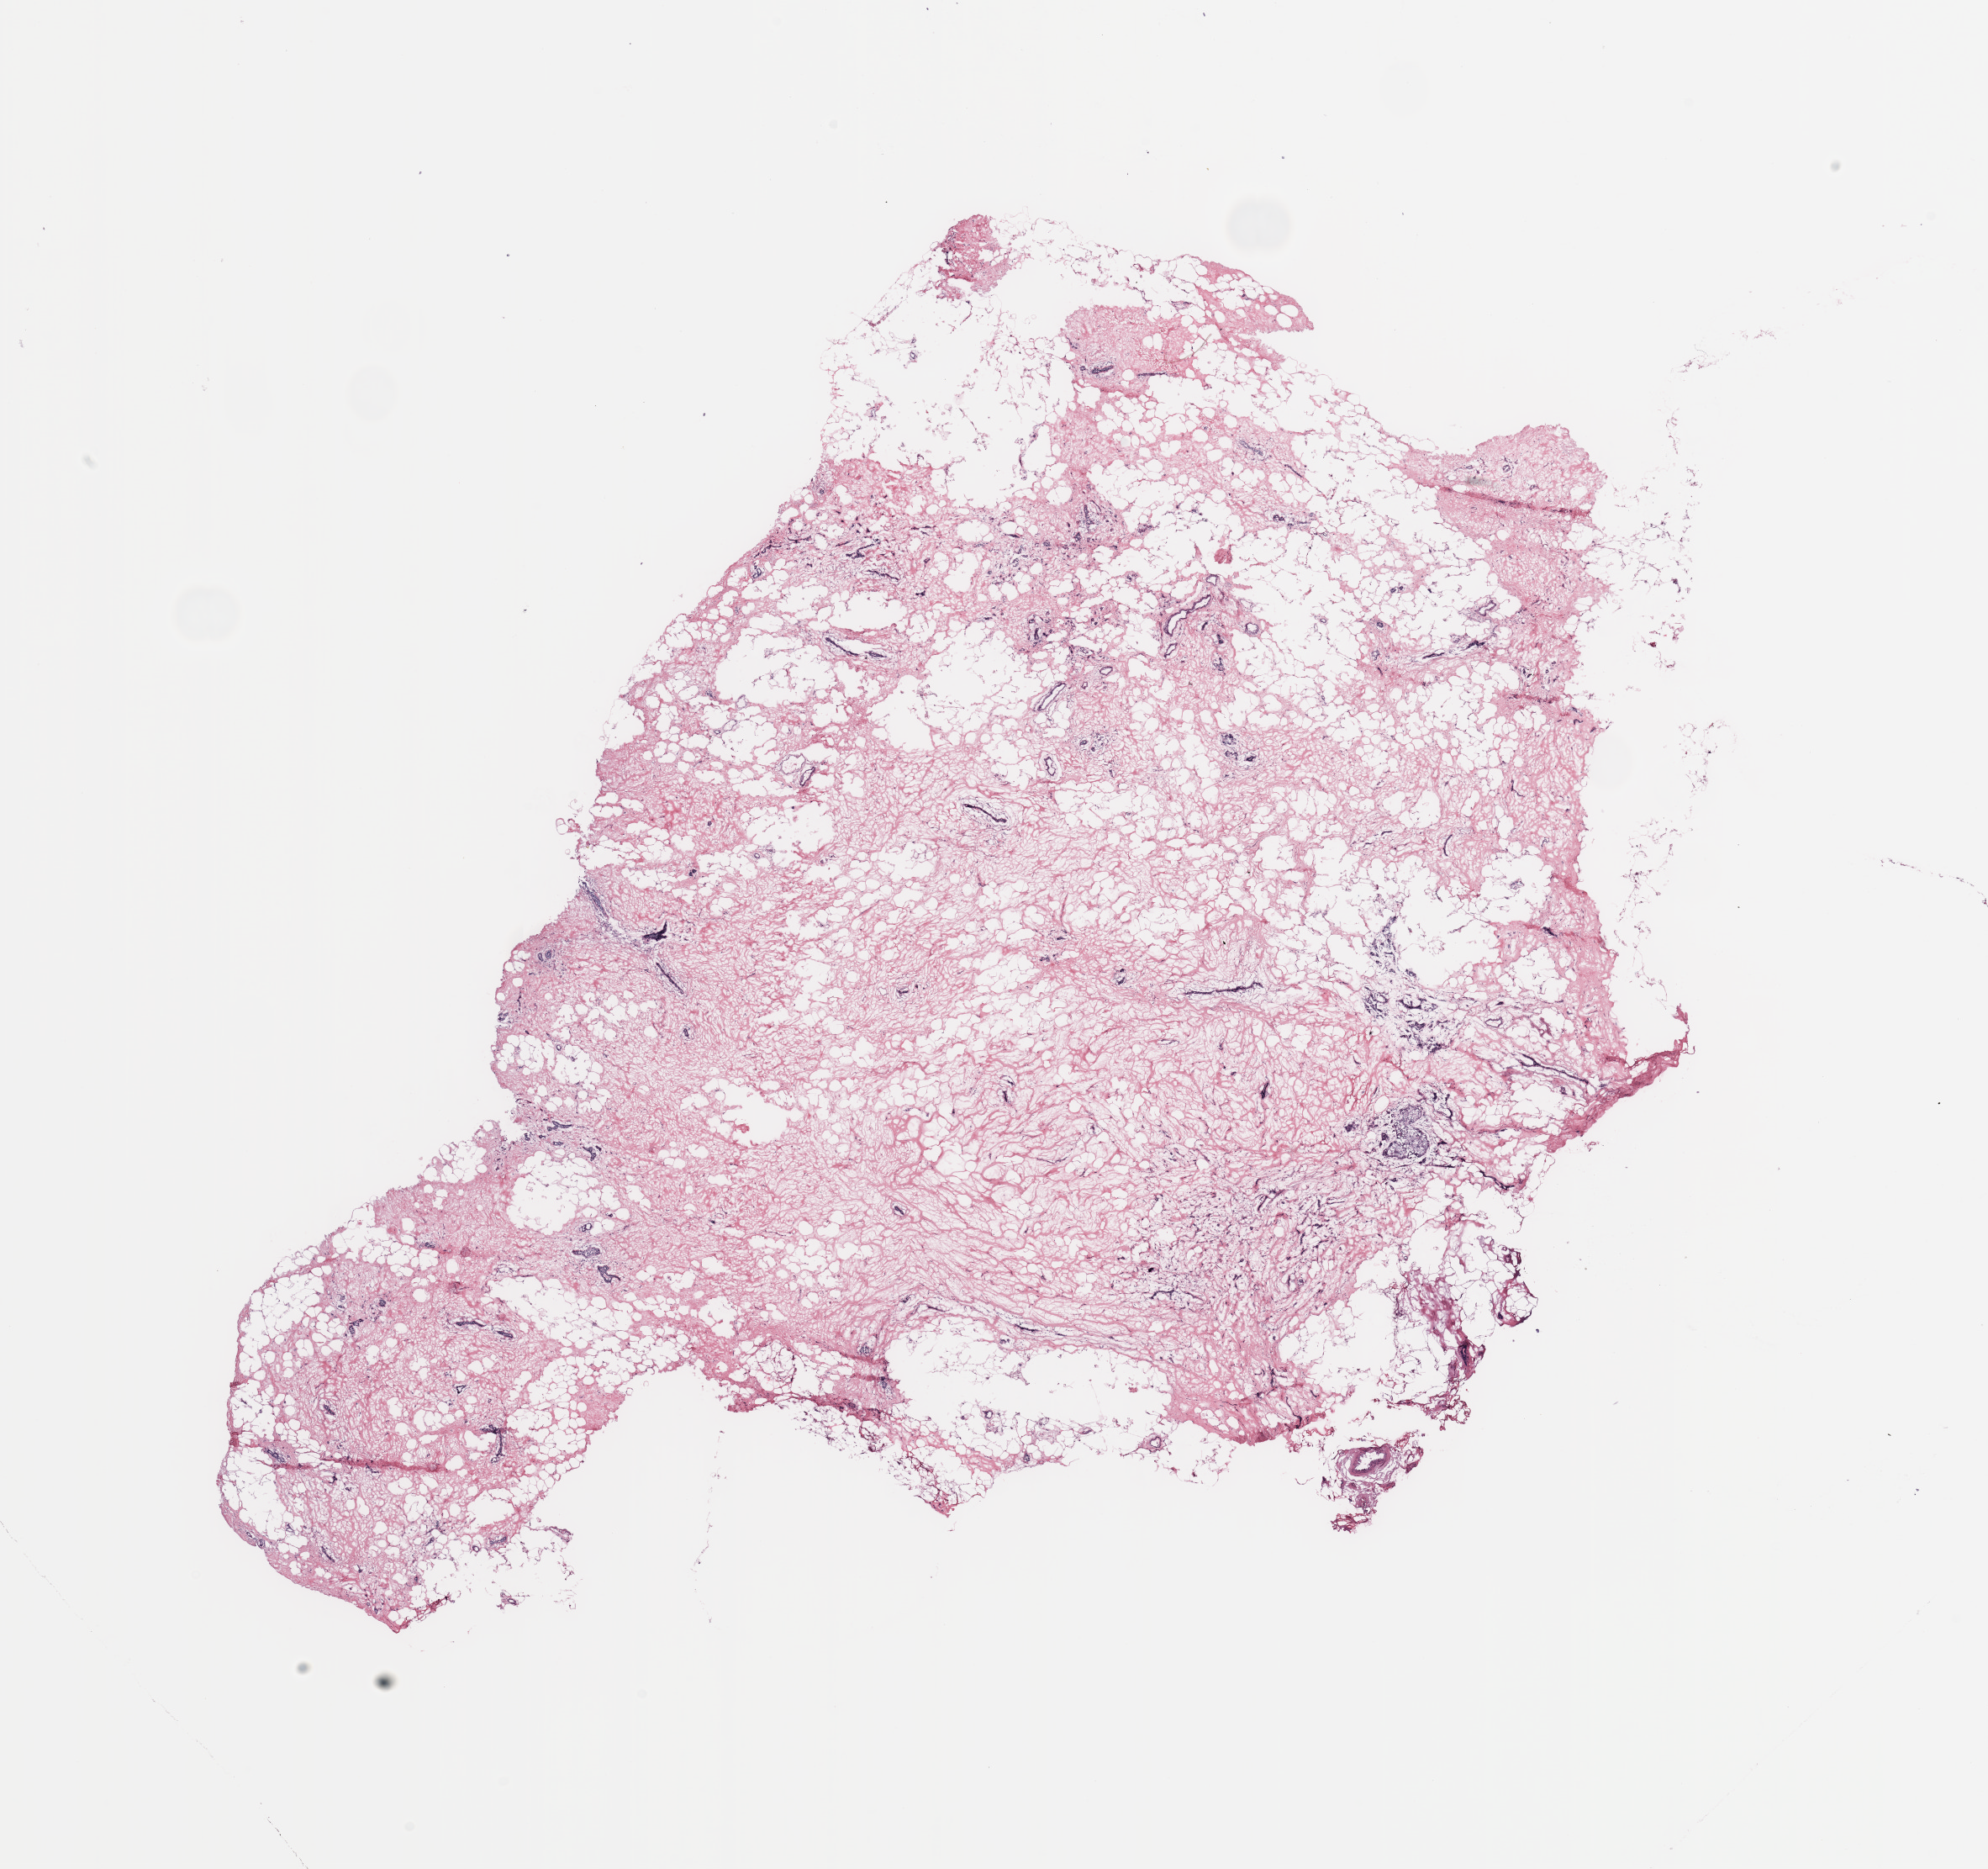
Digitized H&E tissue section (whole slide) — low-resolution overview of the scanned area, about 18.7 x 17.6 mm; breast, tissue type not recorded.
Patient diagnosis (cohort enrolment): breast cancer (breast).